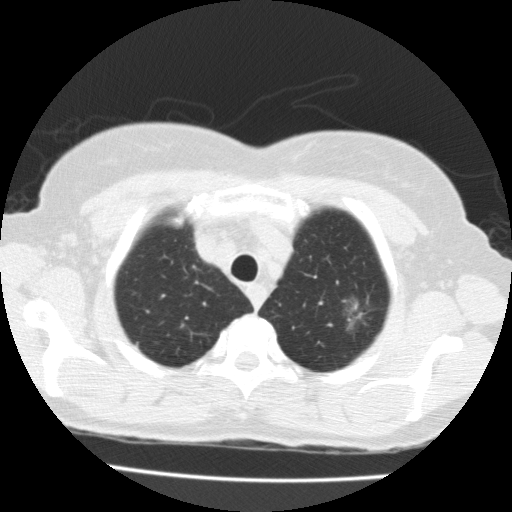
Low-dose screening chest CT, one axial slice; slice 156 of 183 in the series (ordered by position); reconstruction kernel FC10; lung window (W 1500 / L -600 HU); 2 mm slice thickness; 512 × 512 image matrix, field of view 320 × 320 mm.
Annotated regions visible in this slice (expert manual segmentation):
- lesion 1 (tumor, upper lobe of left lung): box from (x=345, y=297) to (x=362, y=319) px